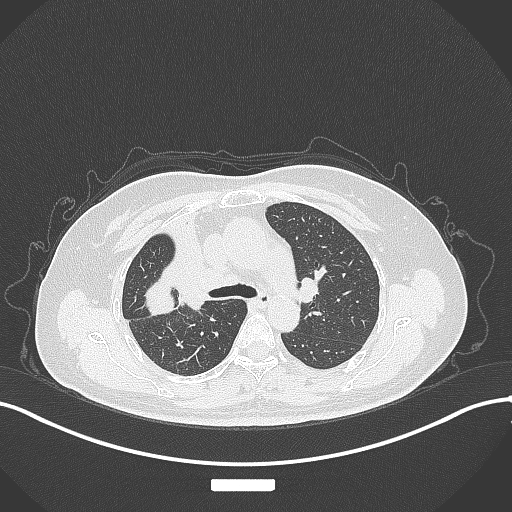
Chest CT, one axial slice. Slice 209 of 309 in the series (ordered by position). Reconstruction kernel B70f. Lung window (W 1500 / L -600 HU). 512 × 512 image matrix. Patient: female, 60 years. Case-level facts recorded for this patient, not image findings: clinical TNM (as recorded): T3 N1 M1.
Structures marked on this image (rectangle marked by the reading radiologist):
- lung tumour (recorded histology: adenocarcinoma): box from (x=134, y=271) to (x=179, y=315) px